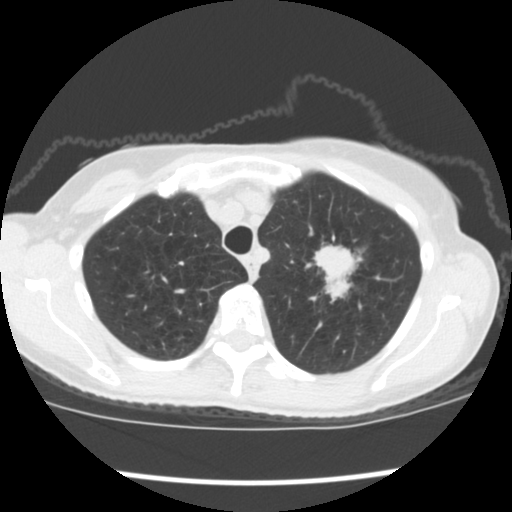
Low-dose screening chest CT, one axial slice; slice 148 of 176 in the series (ordered by position); reconstruction kernel STANDARD; 120 kVp; lung window (W 1500 / L -600 HU); 512 × 512 image matrix.
Structures marked on this image (outlined manually by an expert reader):
- lesion 1 (tumor, upper lobe of left lung): bounding box <314,245,362,301> (left, top, right, bottom; pixels)